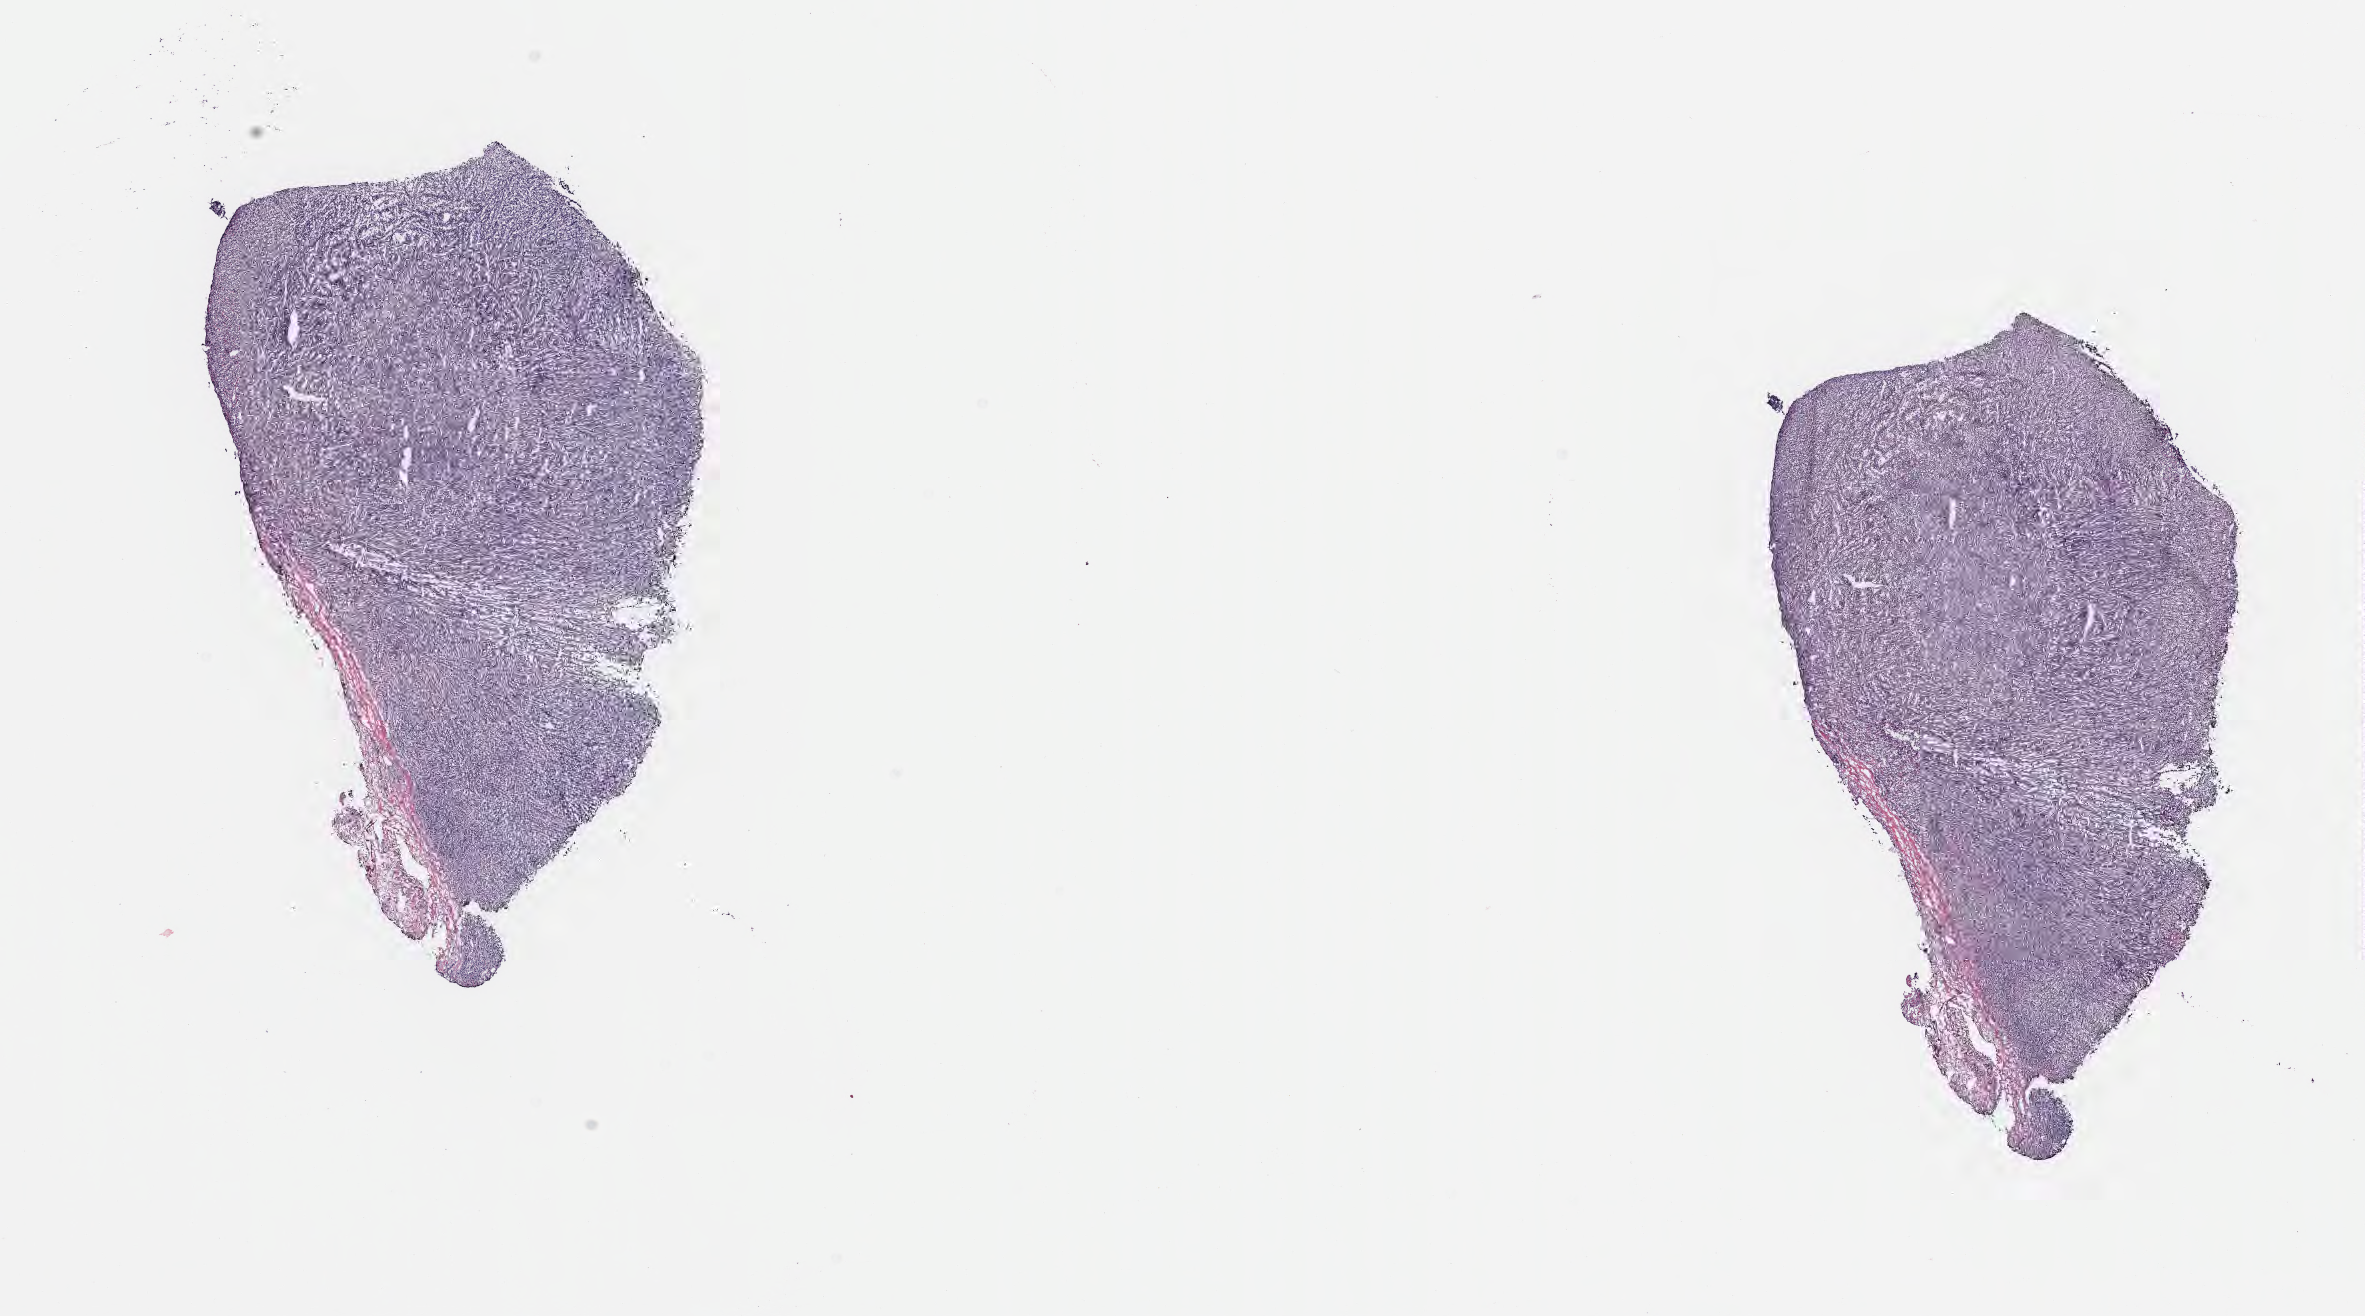
Haematoxylin and eosin whole-slide image, low-resolution overview of the scanned area, about 19.1 x 10.6 mm. Frozen section. Primary tumor. Anatomic site: cranium. Patient: male, age at initial diagnosis 8 years. Pathologist review of this section (percent, as recorded): tumor cells 90%, tumor nuclei 95%, stromal cells 5%, necrosis 0%, normal cells 5%. Inflammatory infiltration, as recorded: lymphocyte infiltration 80%, monocyte infiltration 10%, neutrophil infiltration 5%.
• Ann Arbor stage (patient): Stage IV
• diagnosis: Burkitt lymphoma, NOS